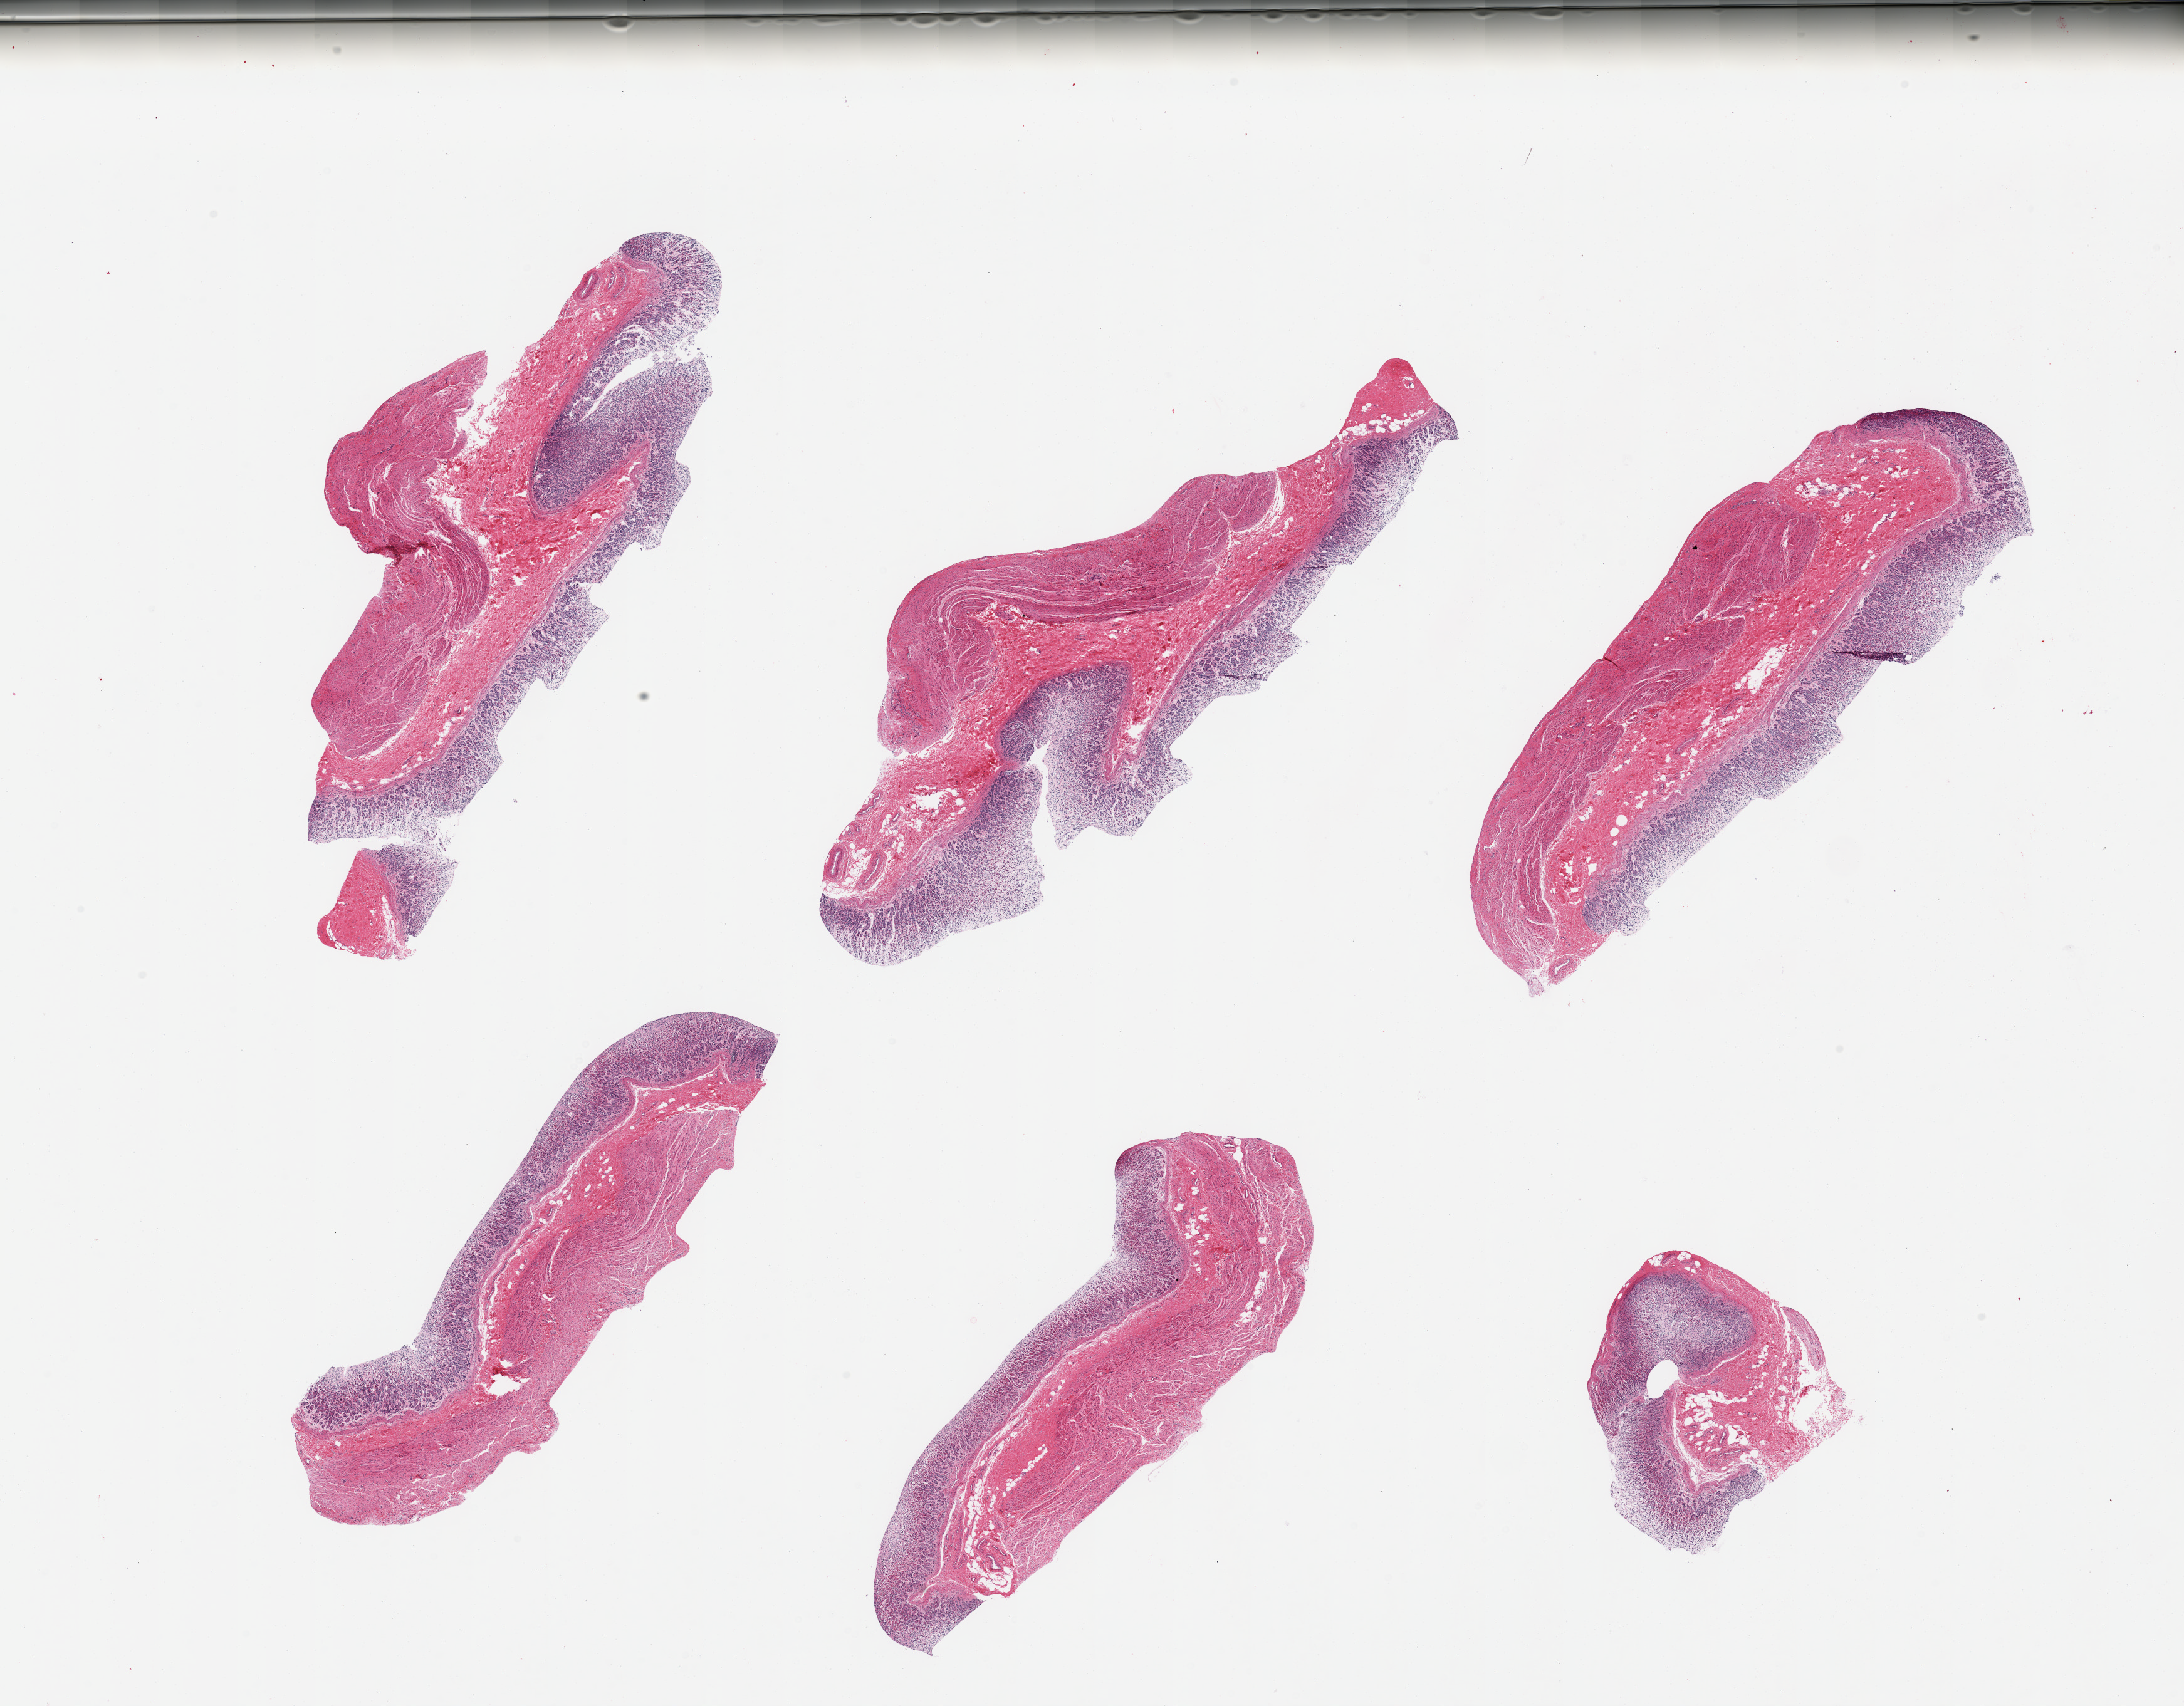
Digitized hematoxylin and eosin (H&E)-stained section, whole scanned area (about 27.6 x 21.5 mm) shown as a low-resolution overview, PAXgene-fixed, paraffin-embedded tissue, sampled site (target tissue): stomach, tissue donor sample.
• review note (as recorded): 6 pieces; mucosa largely autolyzed, muscularis intact